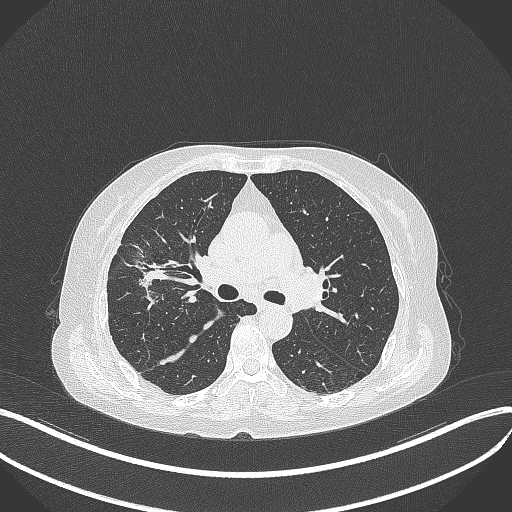
Chest CT, one axial slice. Slice 247 of 429 in the series (ordered by position). Reconstruction kernel B70f. 120 kVp. Lung window (W 1500 / L -600 HU). 1 mm slice thickness. 512 × 512 image matrix, field of view 400 × 400 mm. Female patient, age 69 years. From the clinical record (not read from this slice): clinical TNM (as recorded): T1b N3 M0.
Annotated regions visible in this slice (bounding box drawn by a radiologist):
- lung tumour (recorded histology: small cell carcinoma): bounding box (x1, y1, x2, y2) in pixels: (124, 255, 168, 289)